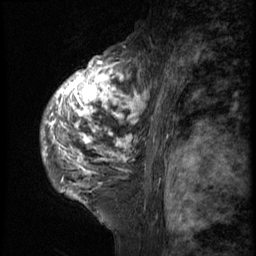
Breast MRI (dynamic contrast-enhanced), one sagittal slice. 3 images stored at this slice position (order not interpretable as contrast timing). 1.5 T. TE 4.2 ms, TR 9 ms. 256 × 256 image matrix. Patient: female, 50 years. From the clinical record (not read from this slice): setting: breast cancer imaged before/during neoadjuvant chemotherapy; receptor status: triple-negative.
Annotated regions visible in this slice (semi-automatic segmentation, software-assisted and operator-edited):
- analysis volume of interest (the breast-tissue region the enhancement analysis was run in; not a lesion): box from (x=41, y=48) to (x=133, y=214) px
- tumour enhancement mask (voxels above the 140 % enhancement threshold inside the analysis volume of interest): (x=44, y=58)–(x=133, y=201)